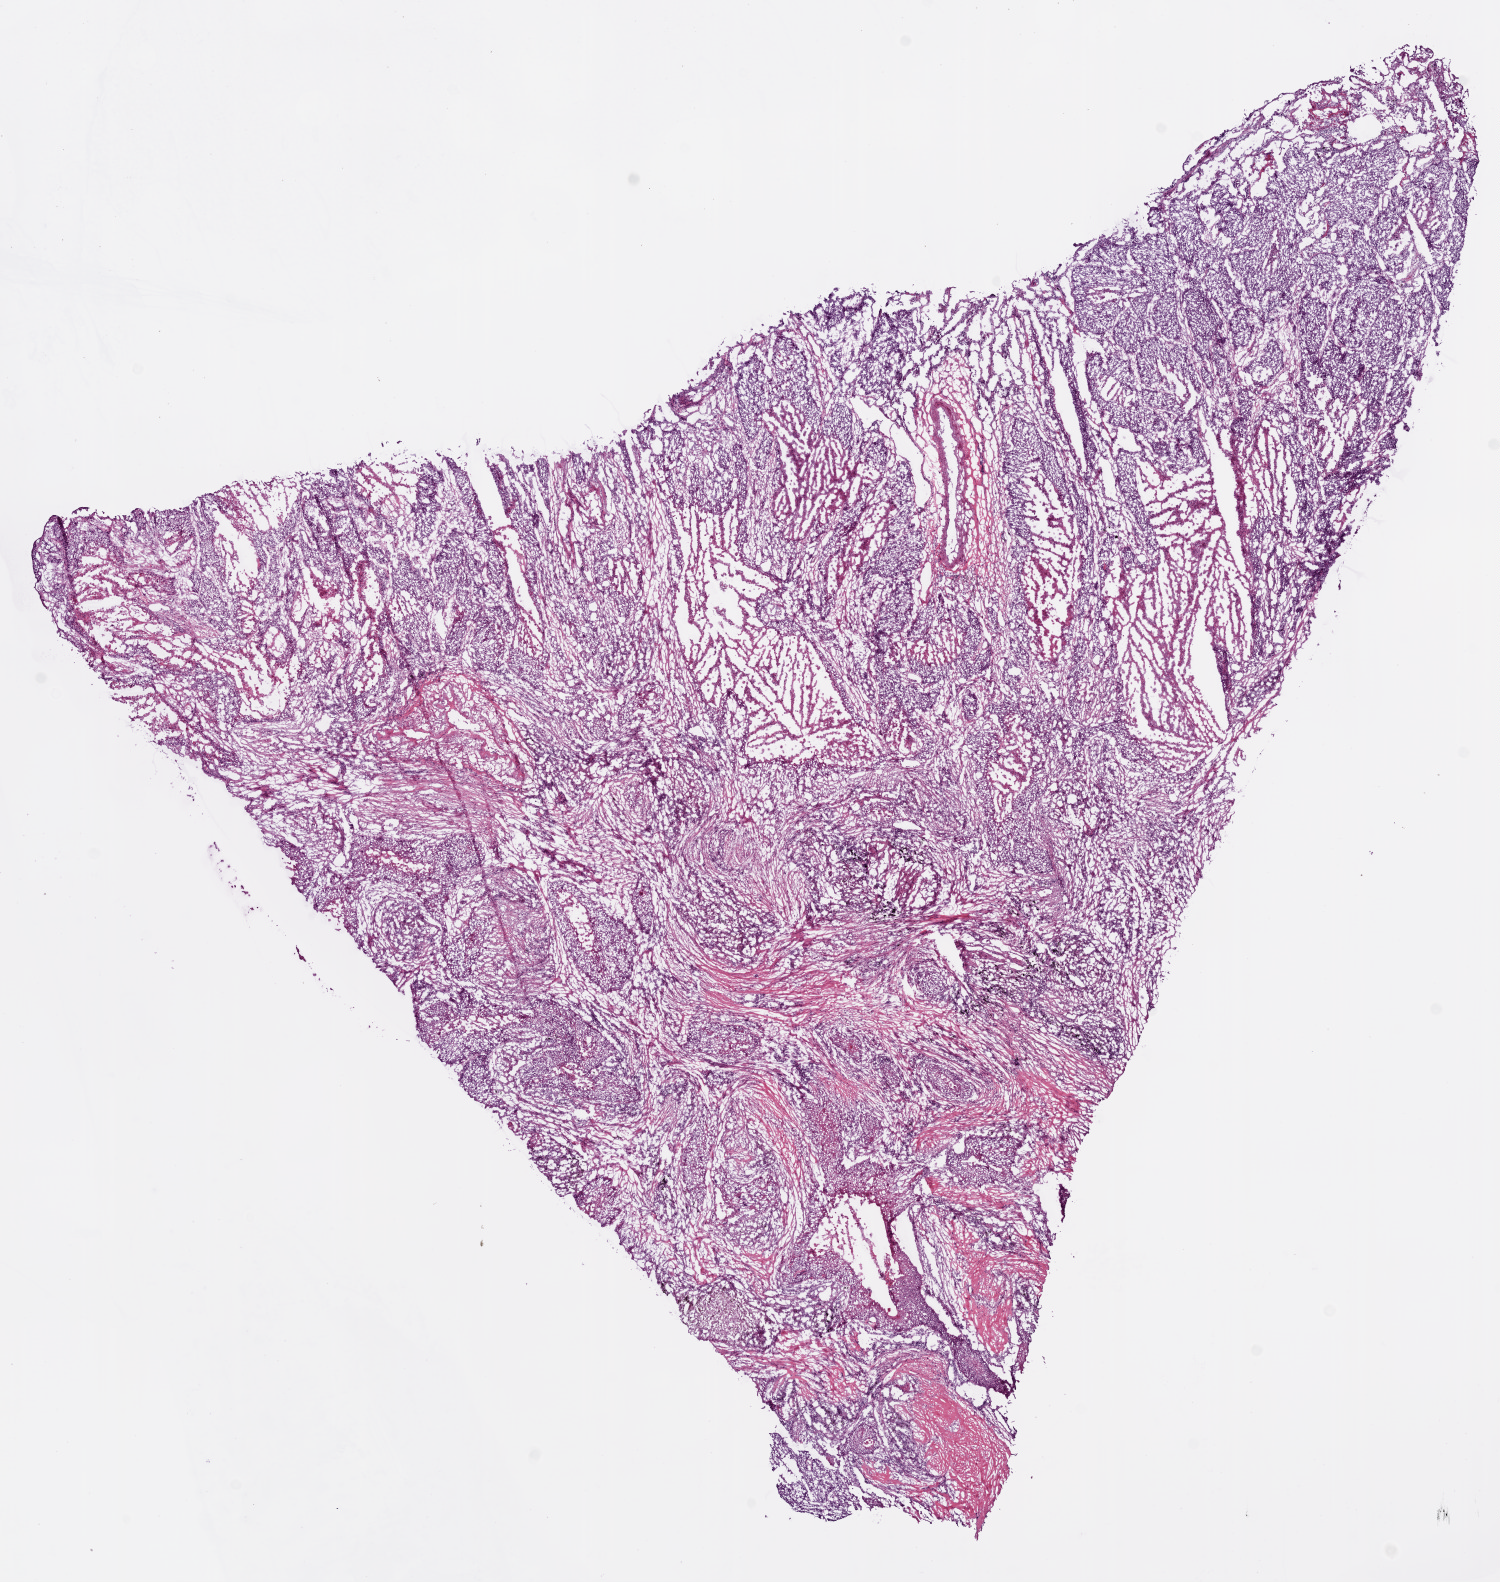
Hematoxylin and eosin (H&E) stained whole-slide image — whole scanned area (about 12.0 x 12.7 mm, from a 20x scan) shown as a low-resolution overview, frozen section from the bottom of the tissue portion, primary tumour sample from the lung. Patient: female, age at initial diagnosis 68 years. Pathologist review of this section (percent, as recorded): tumour cells 77%, tumour nuclei 80%, normal cells 0%, stromal cells 0%, necrosis 23%. Infiltration values recorded for this section: lymphocyte infiltration 5%, monocyte infiltration 5%, neutrophil infiltration 0%.
• diagnosis: Squamous cell carcinoma, NOS (lower lobe, lung)
• AJCC pathologic stage: IB